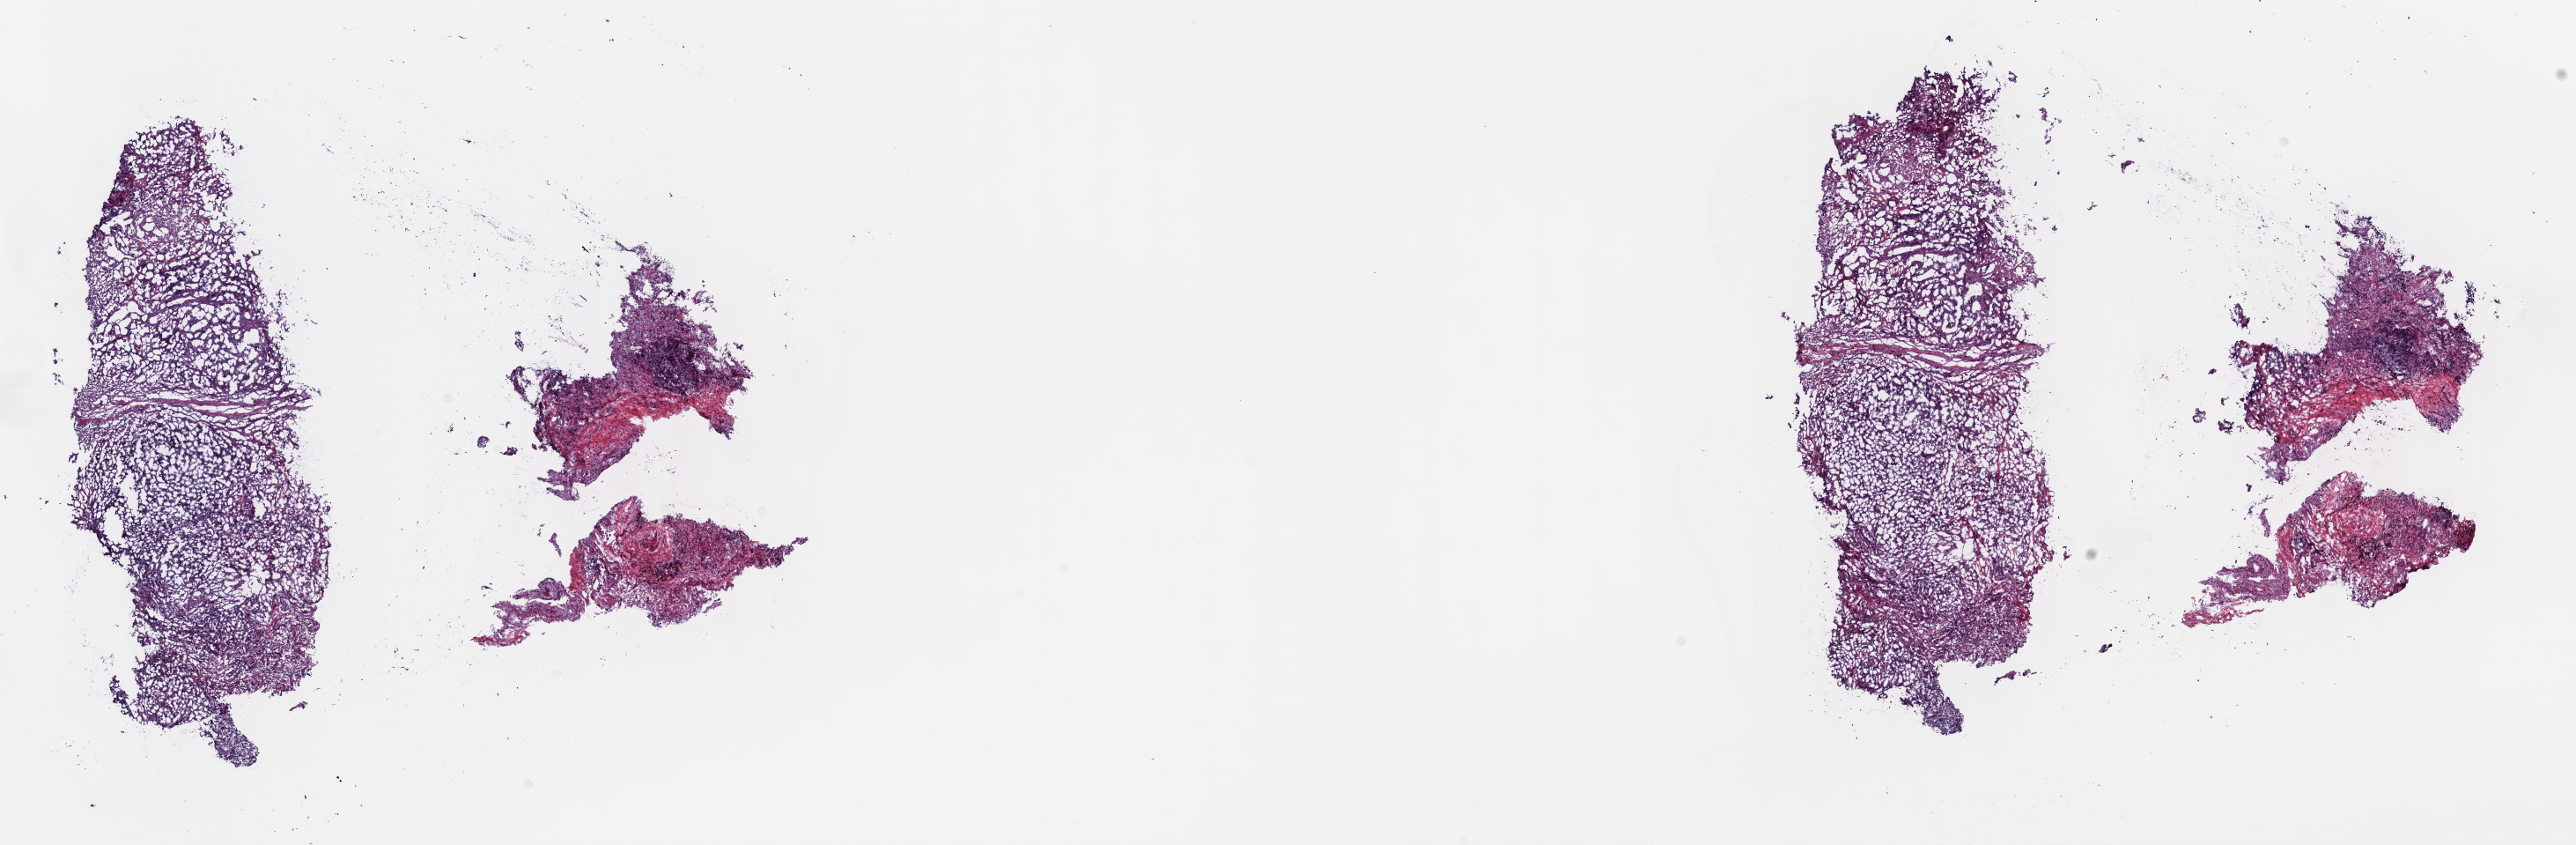
Digitized H&E tissue section (whole slide) — low-resolution overview of the scanned area, about 23.7 x 7.8 mm. Frozen section from the top of the tissue portion. Sample: primary tumour, lung. Male, age 69 years at initial diagnosis.
Pathologic diagnosis: Adenocarcinoma, NOS (upper lobe, lung).